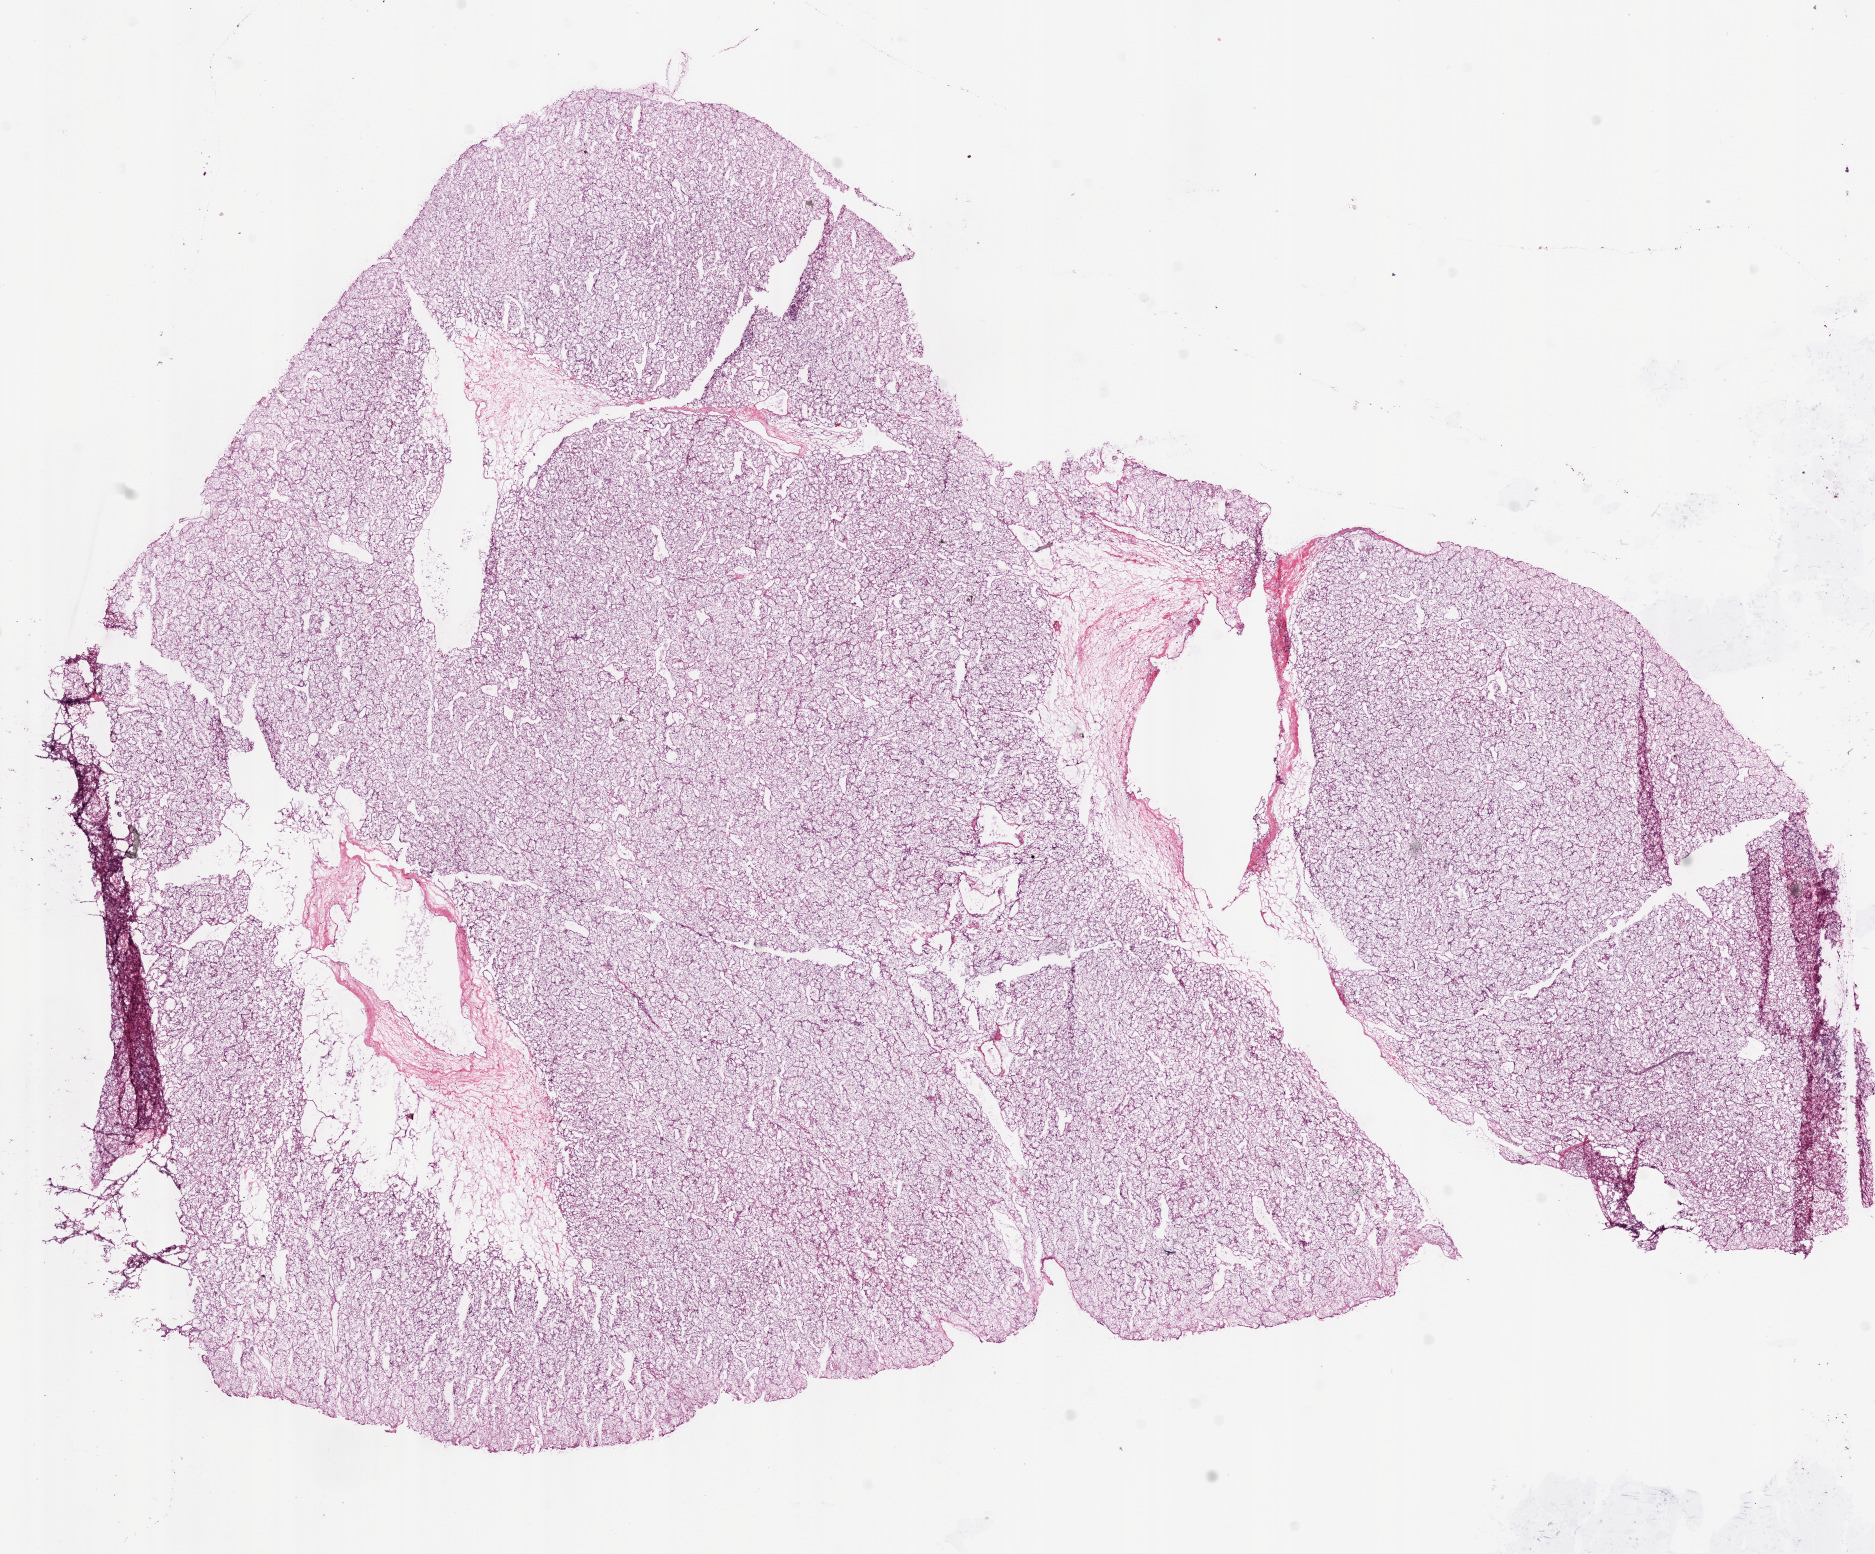
Whole-slide histology image, H&E-stained, shown as a low-resolution overview of the whole scanned area (about 15.0 x 12.5 mm), frozen section, primary tumour sample from the kidney. Patient: male, age at initial diagnosis 69 years. Histologic grade: G2 (moderately differentiated). Pathologist review of this section (percent, as recorded): tumour cells 95%, tumour nuclei 90%, normal cells 0%, stromal cells 5%, necrosis 0%.
Laterality: right. AJCC pathologic stage: I. Lymph nodes positive (case pathology): 0 of 5 examined. Histologic diagnosis: Clear cell adenocarcinoma, NOS.